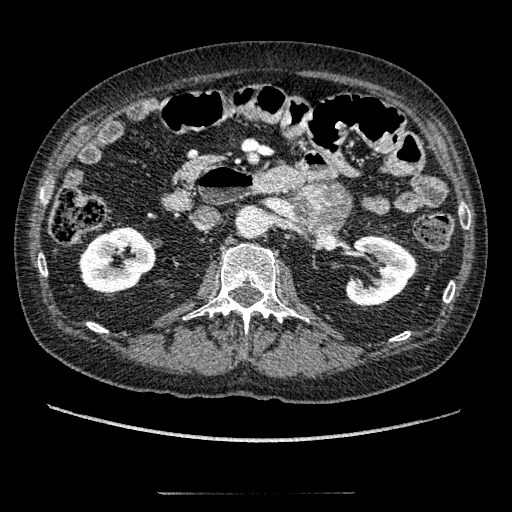
Contrast-enhanced abdominal CT, one axial slice. Slice 86 of 274 in the series (ordered by position). Reconstruction kernel STANDARD. Intravenous contrast given. Soft-tissue window (W 400 / L 40 HU). 1.25 mm slice thickness. 512 × 512 image matrix, field of view 381 × 381 mm. Male patient, age 69 years. Case-level facts recorded for this patient, not image findings: diagnosis: adrenocortical carcinoma; tumour side: left adrenal; tumour size at pathology: 6.1 cm; Ki-67 index: 10 %; stage (as recorded): 3.
Annotated regions visible in this slice (semi-automatic segmentation, software-assisted and operator-edited):
- mass: bounding box (x1, y1, x2, y2) in pixels: (298, 185, 348, 225)